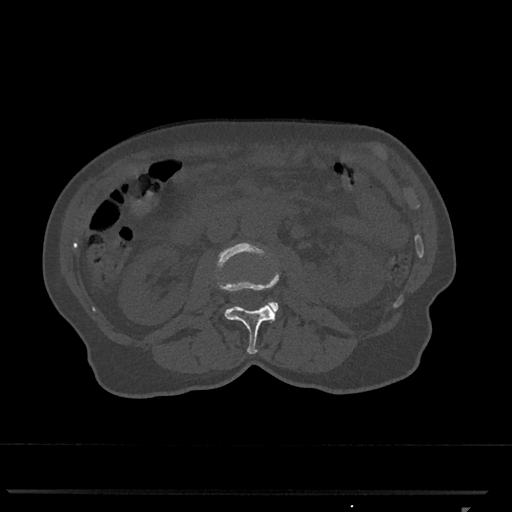
CT including the spine, one axial slice. Slice 318 of 793 in the series (ordered by position). Reconstruction kernel Br40s/3. 120 kVp. Bone window (W 1800 / L 400 HU). 0.5 mm slice thickness. 512 × 512 image matrix. Patient: female, 62 years. From the clinical record (not read from this slice): primary cancer: renal.
Annotated regions visible in this slice (semi-automatic segmentation, software-assisted and operator-edited):
- L2 vertebra: box from (x=216, y=242) to (x=280, y=354) px
- L3 vertebra: (x=268, y=302)–(x=279, y=311)